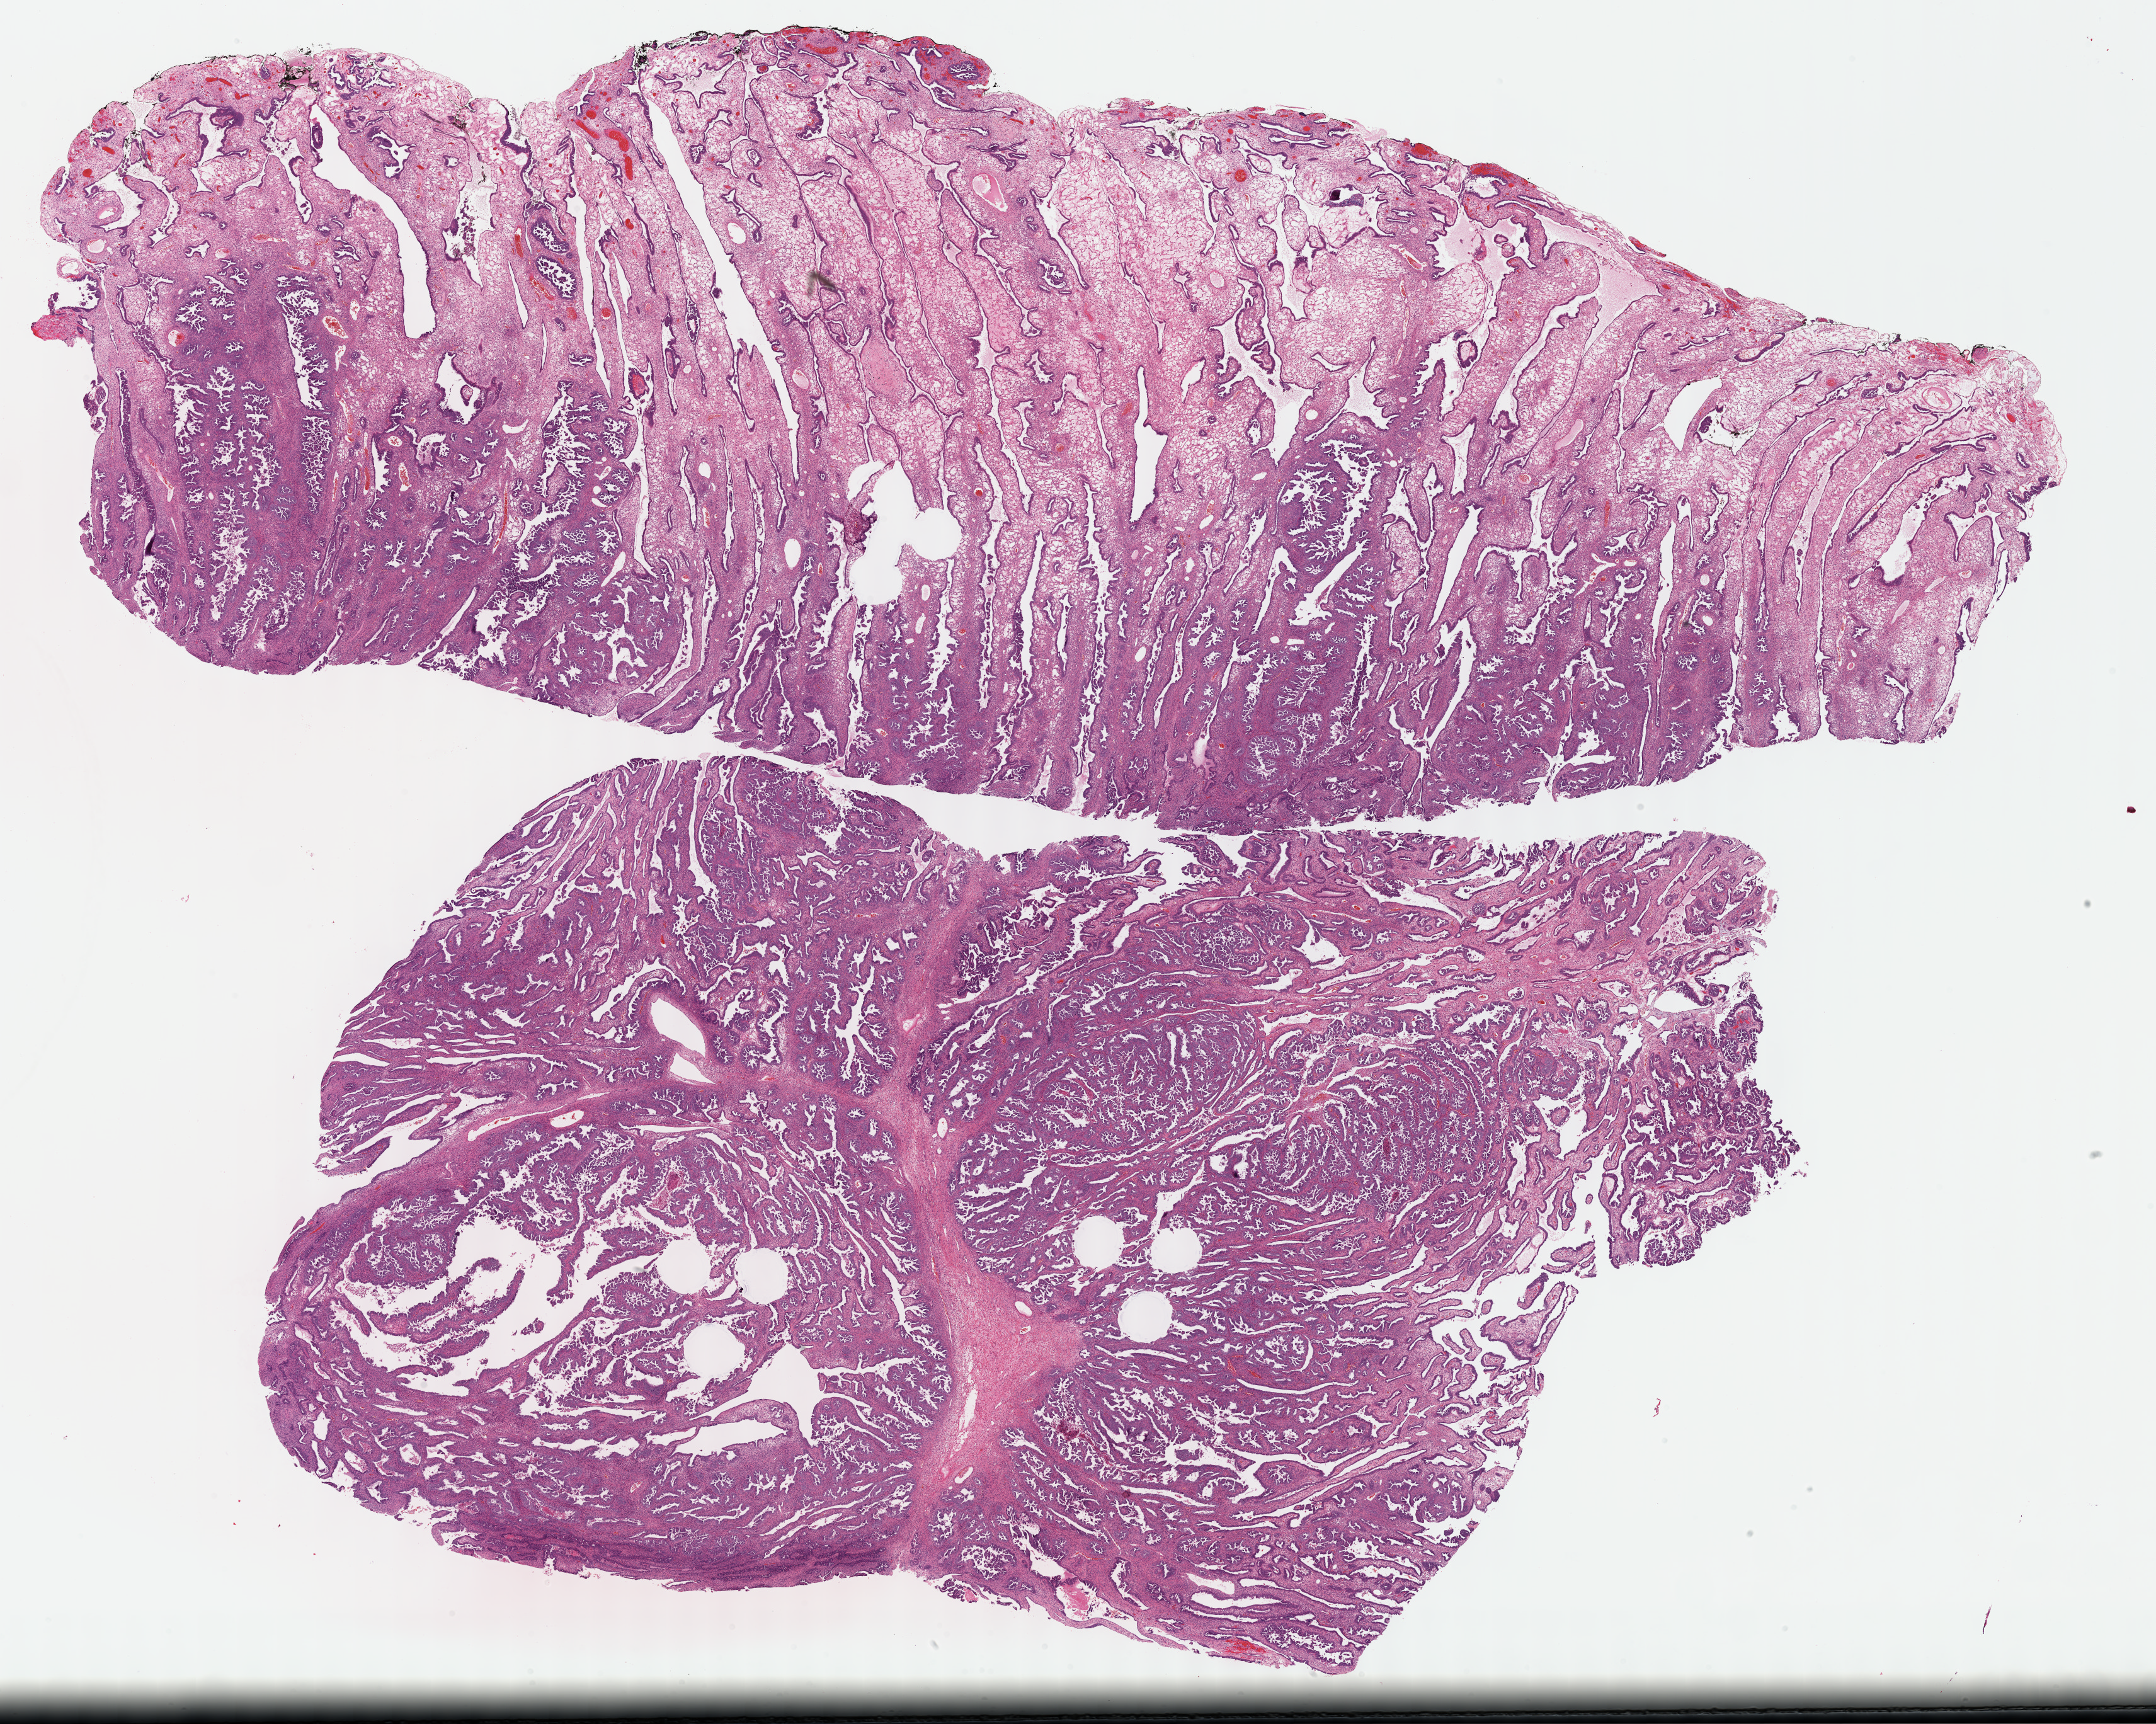
H&E-stained whole-slide image — low-resolution overview of the scanned area, about 27.7 x 22.1 mm; formalin-fixed paraffin-embedded (FFPE) diagnostic section; sample: primary tumour, ovary. Female patient; age at initial diagnosis 52 years. Histologic grade: G3 (poorly differentiated).
• FIGO stage: IV
• histologic diagnosis: Serous cystadenocarcinoma, NOS